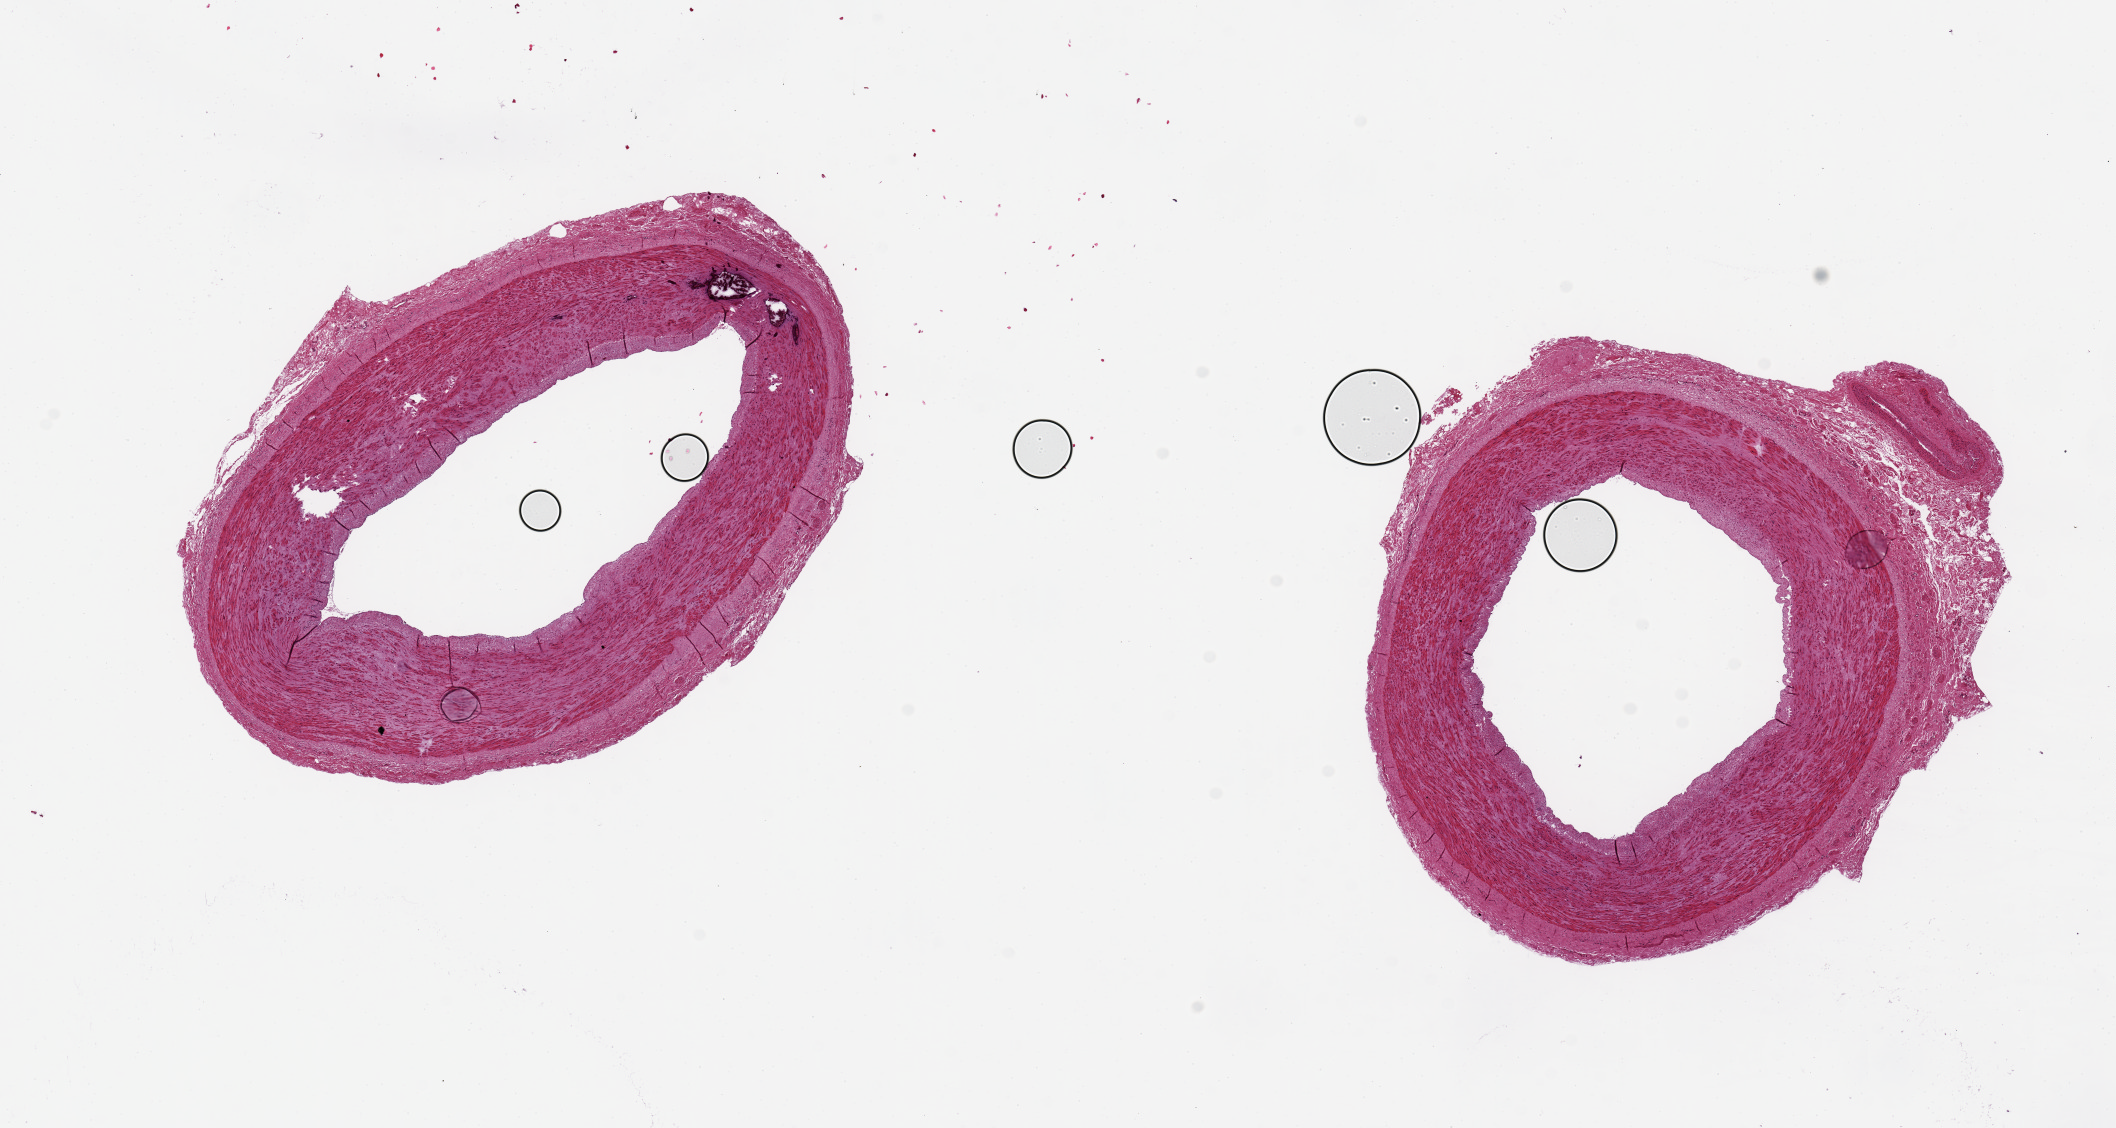
H&E whole-slide image — shown as a low-resolution overview of the whole scanned area (about 16.7 x 8.9 mm, acquisition: 20x scan). PAXgene-fixed paraffin-embedded (PFPE) section. Sampled site (target tissue): tibial artery. Donor tissue sample. Male donor.
* reviewer comment on this tissue sample: 2 pieces, 3.9x5.6 & 5.5x4.7 mm; focal medial calcification in one piece; small vein at periphery of other piece; clean of extraneous adipose